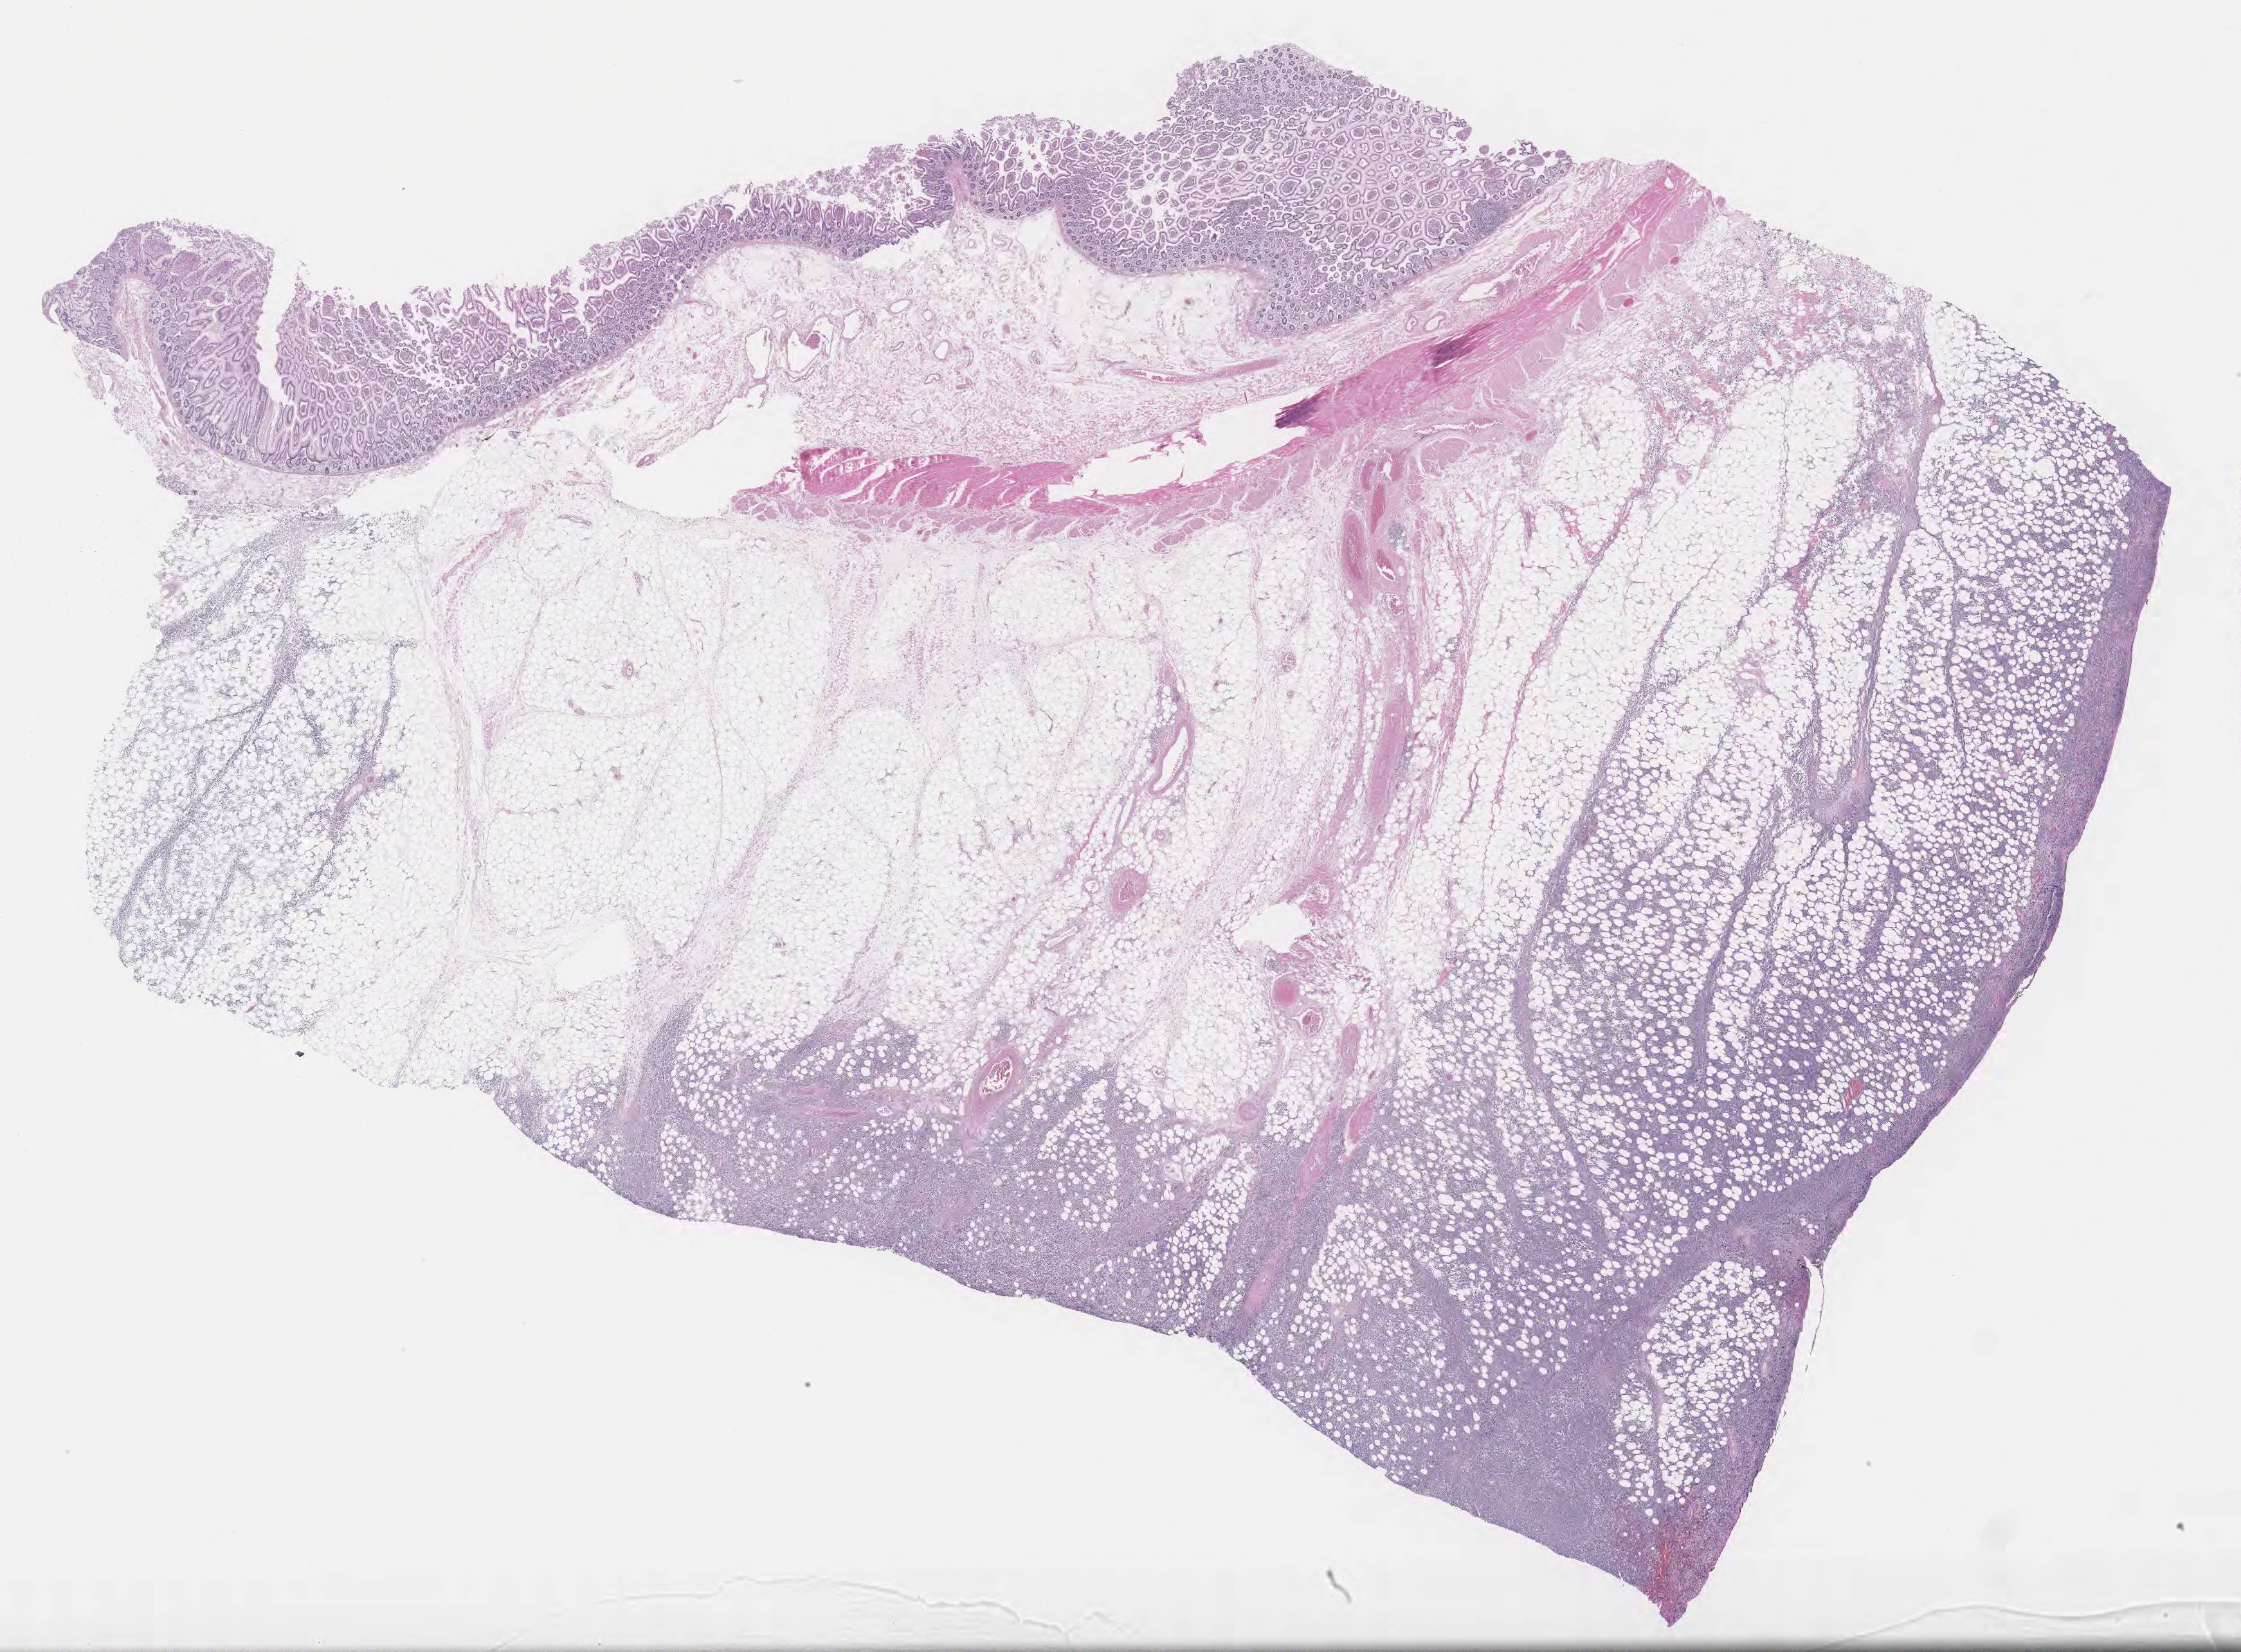
Whole-slide image, H&E stain — whole scanned area (about 28.2 x 20.8 mm) shown as a low-resolution overview. Specimen: tumor tissue. Site: colon. Patient male; aged 63.
Diagnosis: Burkitt lymphoma, NOS.